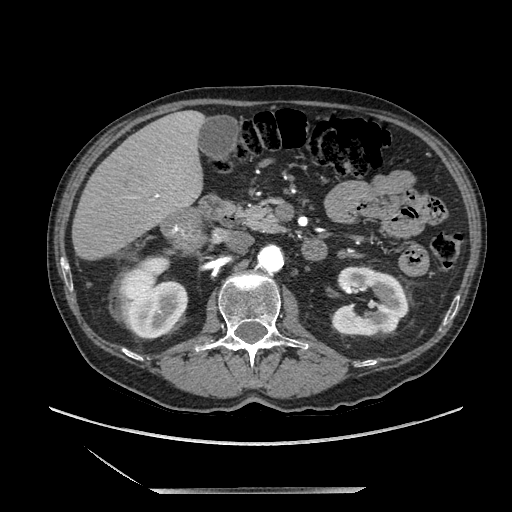
Contrast-enhanced abdominal CT, one axial slice; position 95 of 243 along the scan axis; soft-tissue window (W 400 / L 40 HU); 512 × 512 image matrix. Male patient. Case-level facts recorded for this patient, not image findings: diagnosis: adrenocortical carcinoma; tumour side: right adrenal; tumour size at pathology: 16 cm; Ki-67 index: 17 %; stage (as recorded): 3.
Outlined on this slice (semi-automatically segmented with operator editing):
- mass: bounding box <162,211,204,248> (left, top, right, bottom; pixels)